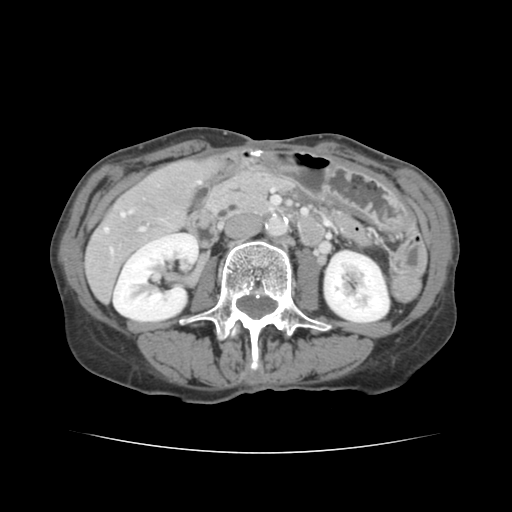
Contrast-enhanced abdominal CT, one axial slice; position 47 of 136 along the scan axis; 120 kVp; intravenous contrast given; soft-tissue window (W 400 / L 40 HU); 2.5 mm slice thickness; 512 × 512 image matrix, field of view 319 × 319 mm. Female patient, age 77 years. Case-level facts recorded for this patient, not image findings: diagnosis: colorectal cancer liver metastases, imaged before liver resection; multiple liver metastases: yes; largest metastasis: 3 cm.
Outlined on this slice (expert manual segmentation):
- hepatic veins: bounding box <105,181,200,252> (left, top, right, bottom; pixels)
- liver: <87,159,213,300>
- planned liver remnant (the part of the liver to remain after resection): <171,160,216,191>
- portal vein (with intrahepatic branches): <126,212,145,231>